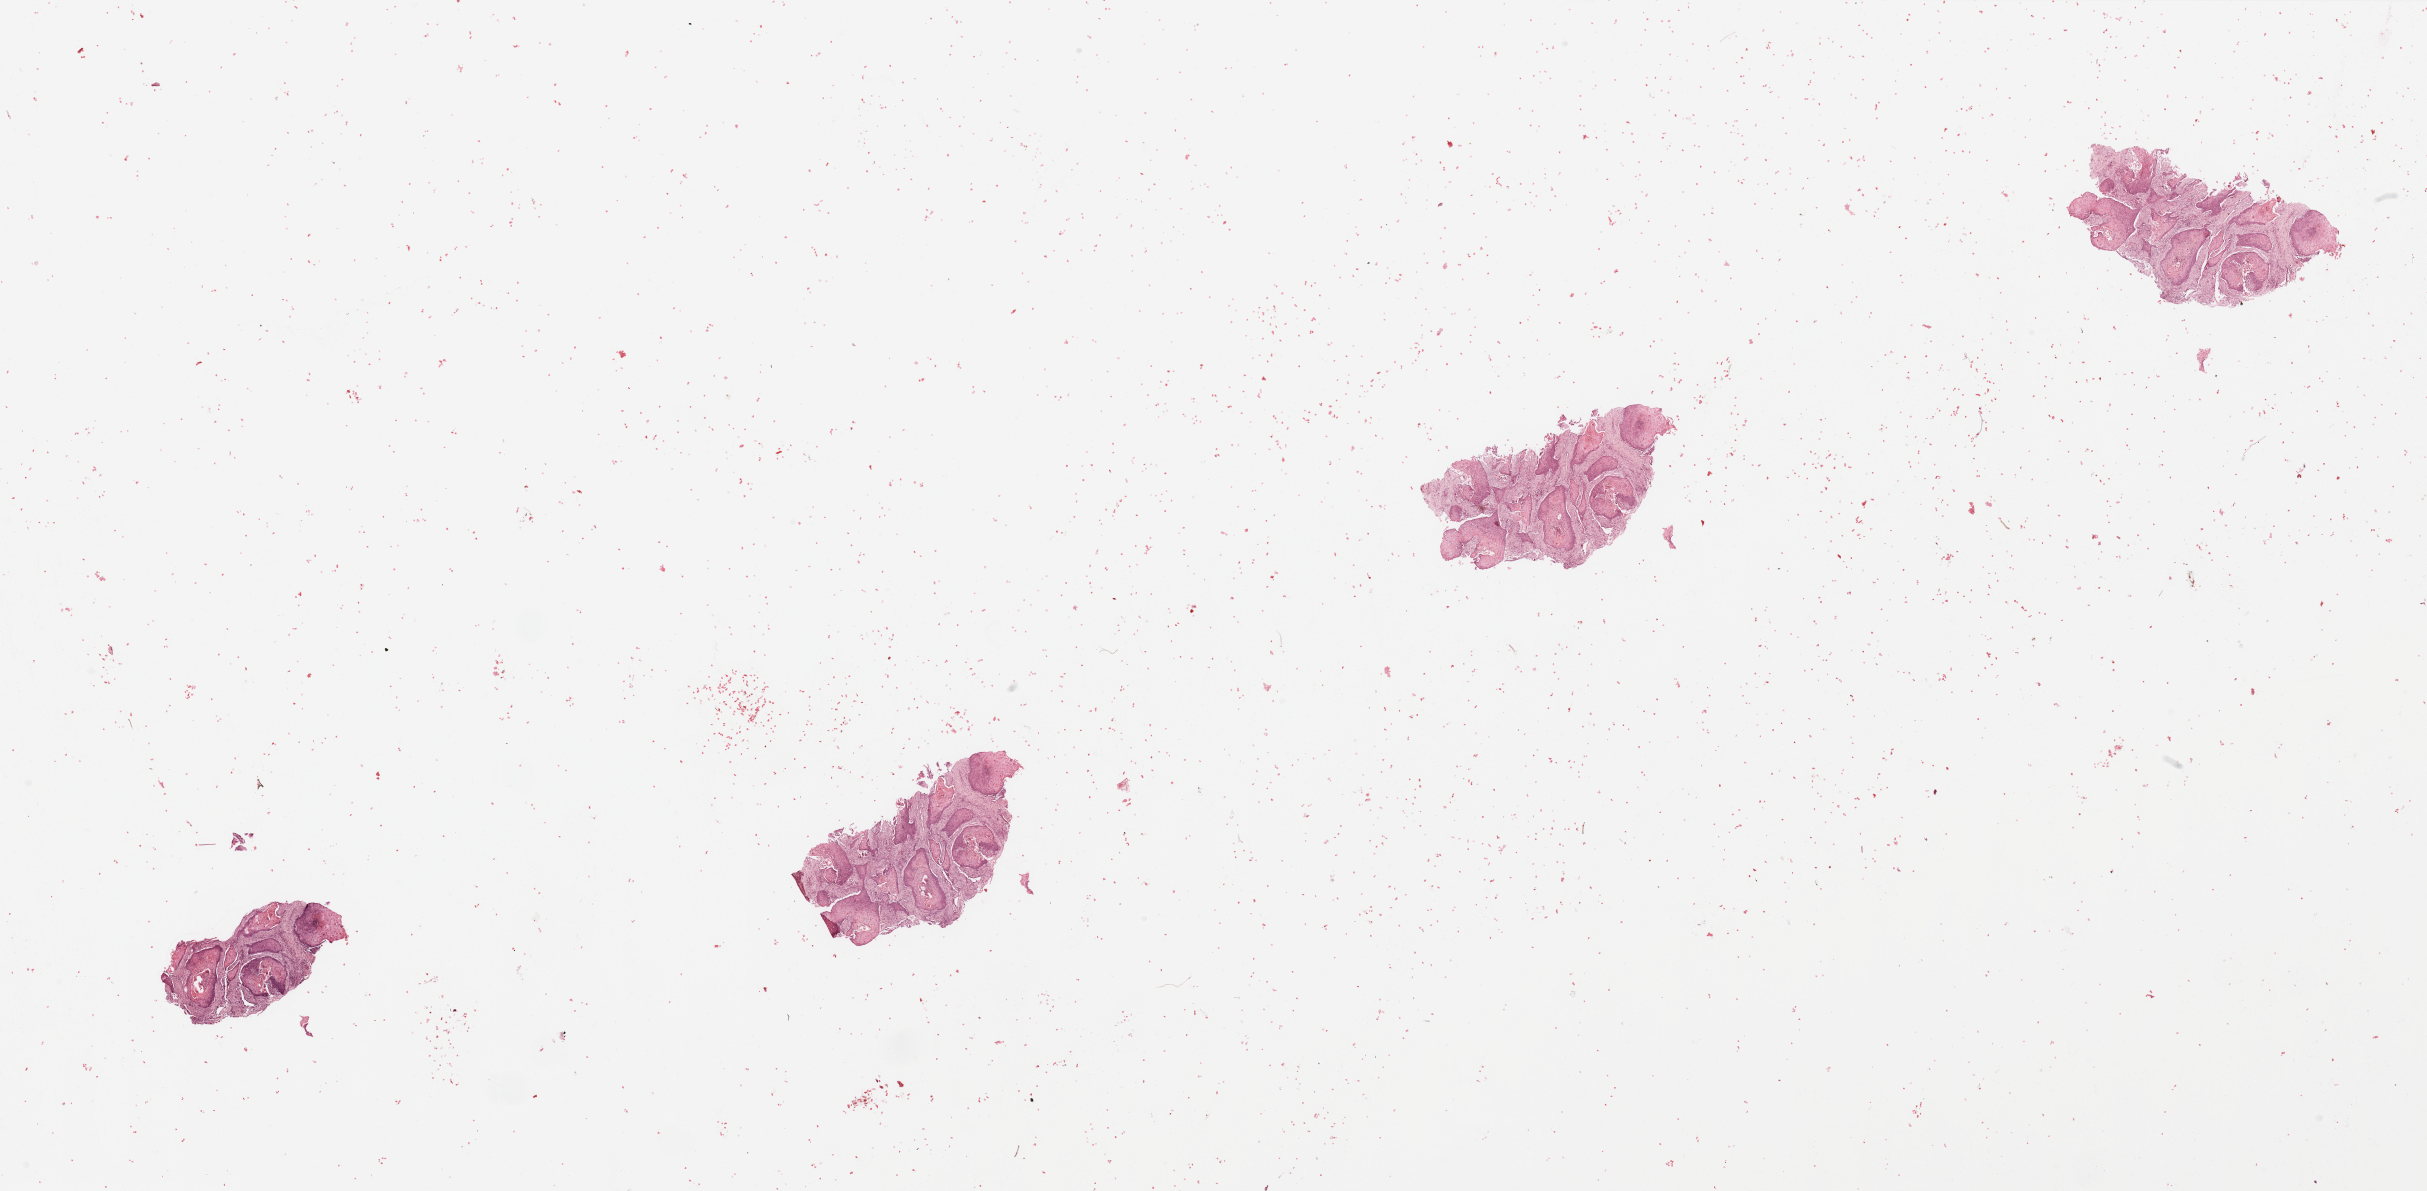
Hematoxylin and eosin (H&E) stained whole-slide image — shown as a low-resolution overview of the whole scanned area (about 38.4 x 18.8 mm, acquisition: 20x scan), tumour tissue sample, sampled site: larynx. Male, 56 y/o. Histologic grade: G2 (moderately differentiated). Pathologist review of this section (percent, as recorded): tumour nuclei 80%, necrosis 2%.
Diagnosis: Squamous cell carcinoma, NOS (larynx, NOS). Primary tumour site (as recorded): larynx. AJCC pathologic stage: III.